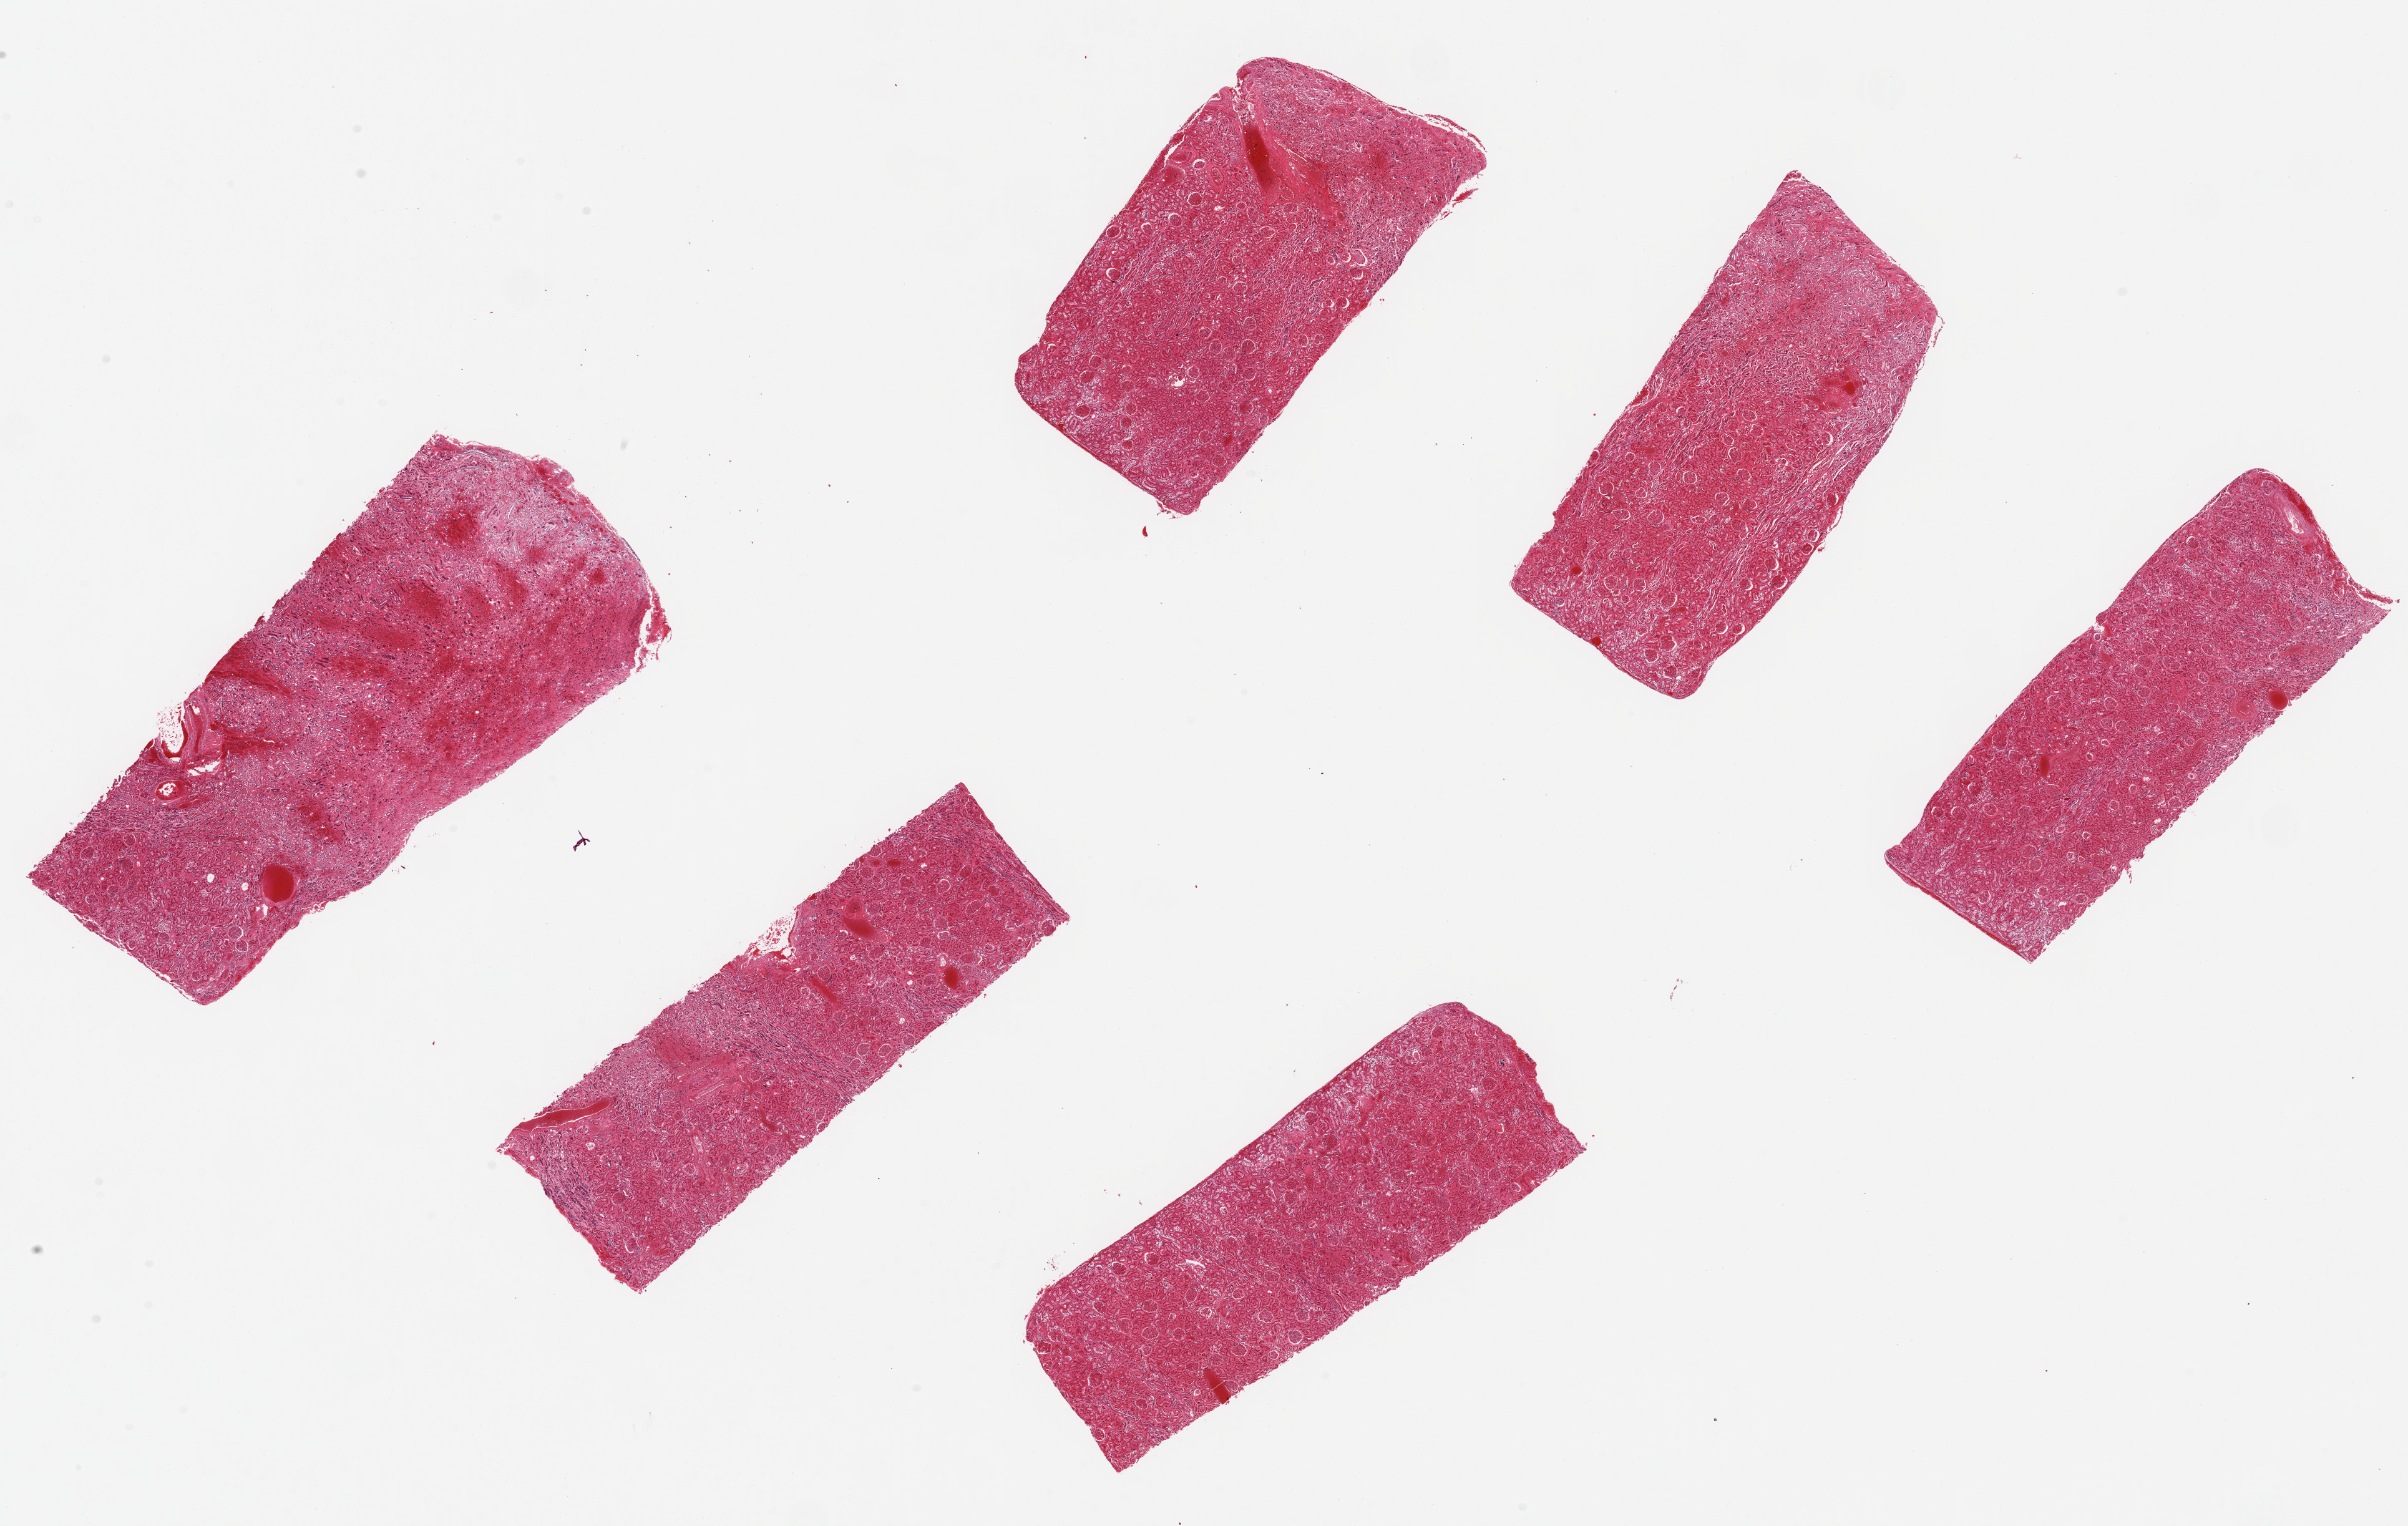
H&E whole-slide image — low-resolution overview of the scanned area, about 30.5 x 19.3 mm (acquisition: 20x scan); PAXgene-fixed, paraffin-embedded tissue; section of renal cortex (target tissue); tissue donor sample. Donor: female.
Review note (as recorded): 6 pieces up to 8x4 mm; 1 piece has 20% cortex and 80% medulla; moderate congestion.